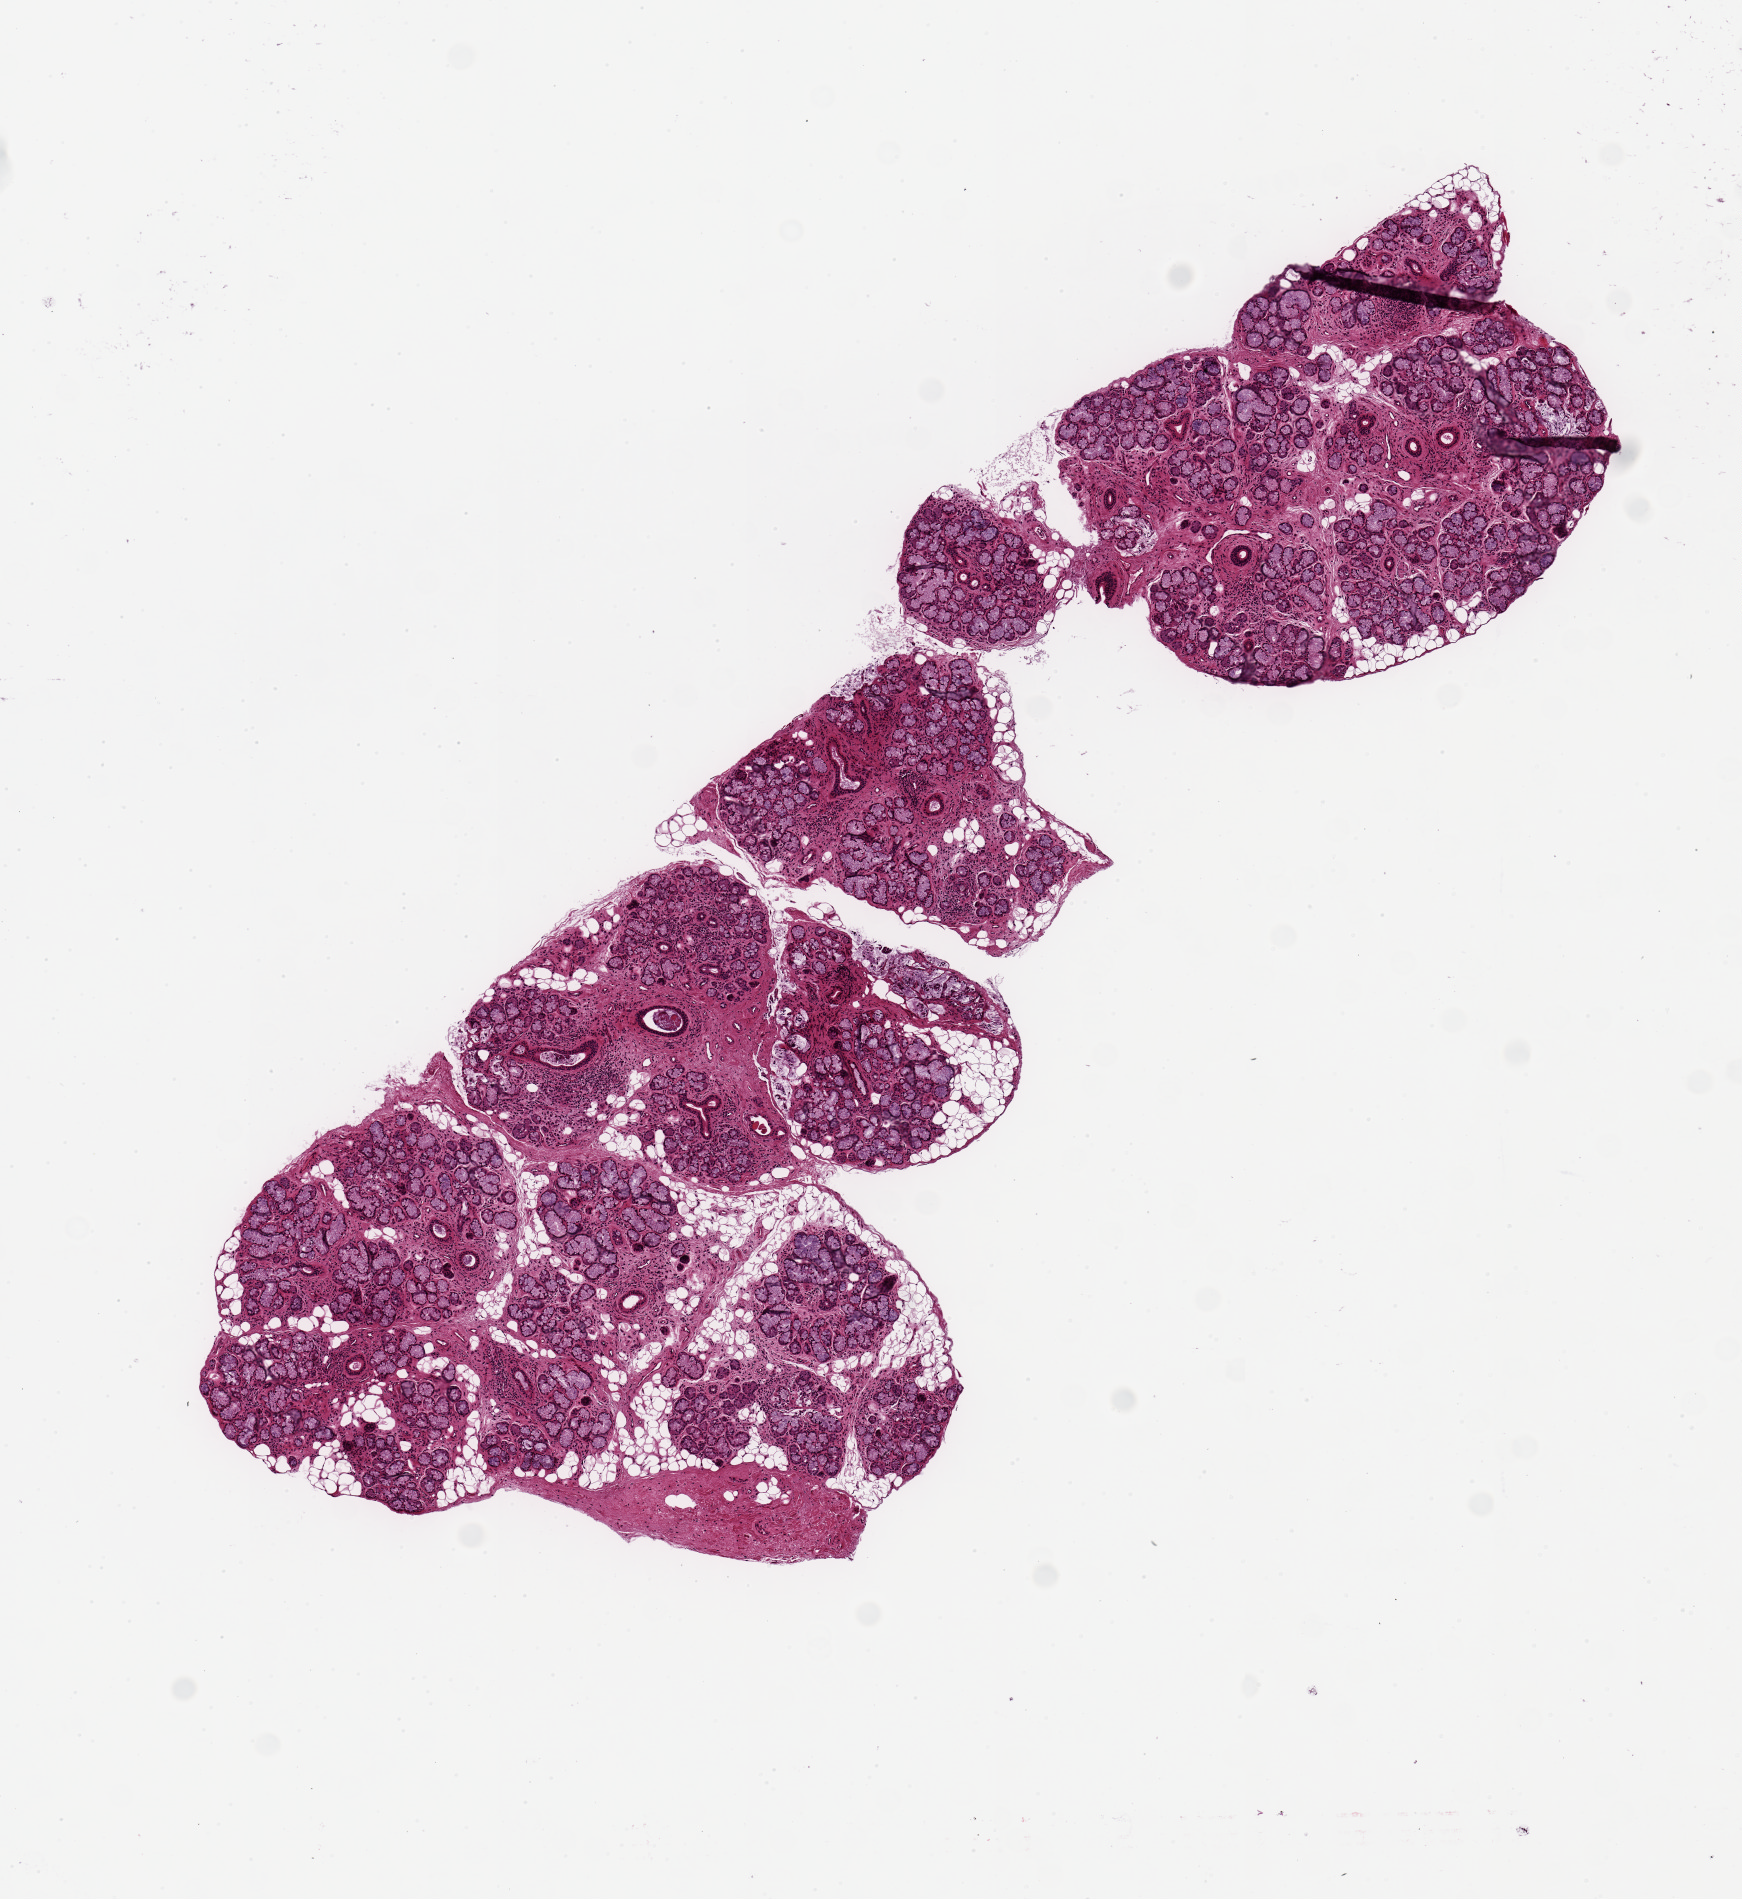
Whole-slide image, hematoxylin and eosin (H&E) stain, shown as a low-resolution overview of the whole scanned area (about 6.9 x 7.5 mm, slide scanned at 20x); PAXgene-fixed paraffin-embedded (PFPE) section; target tissue: minor salivary gland; tissue donor sample.
Reviewer comment on this tissue sample: 1 piece, 7x3mm; well dissected, well preserved; 10% intraglandular adipose.